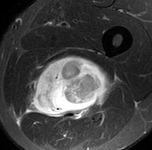
MRI of an extremity soft-tissue mass, one axial slice; position 75 of 90 along the scan axis; STIR; MR volume resampled by the dataset authors to the PET/CT grid (not the native acquisition matrix); 152 × 150 image matrix, field of view 148 × 146 mm. Male patient. Case-level facts recorded for this patient, not image findings: histological type: undifferentiated pleomorphic liposarcoma; grade: high; site of the primary tumour: left thigh.
Outlined on this slice (expert contour drawn on MRI and transferred to this co-registered scan by the dataset authors):
- gross tumour volume including surrounding oedema: box from (x=25, y=53) to (x=117, y=124) px
- gross tumour volume (mass): (x=34, y=57)–(x=115, y=115)